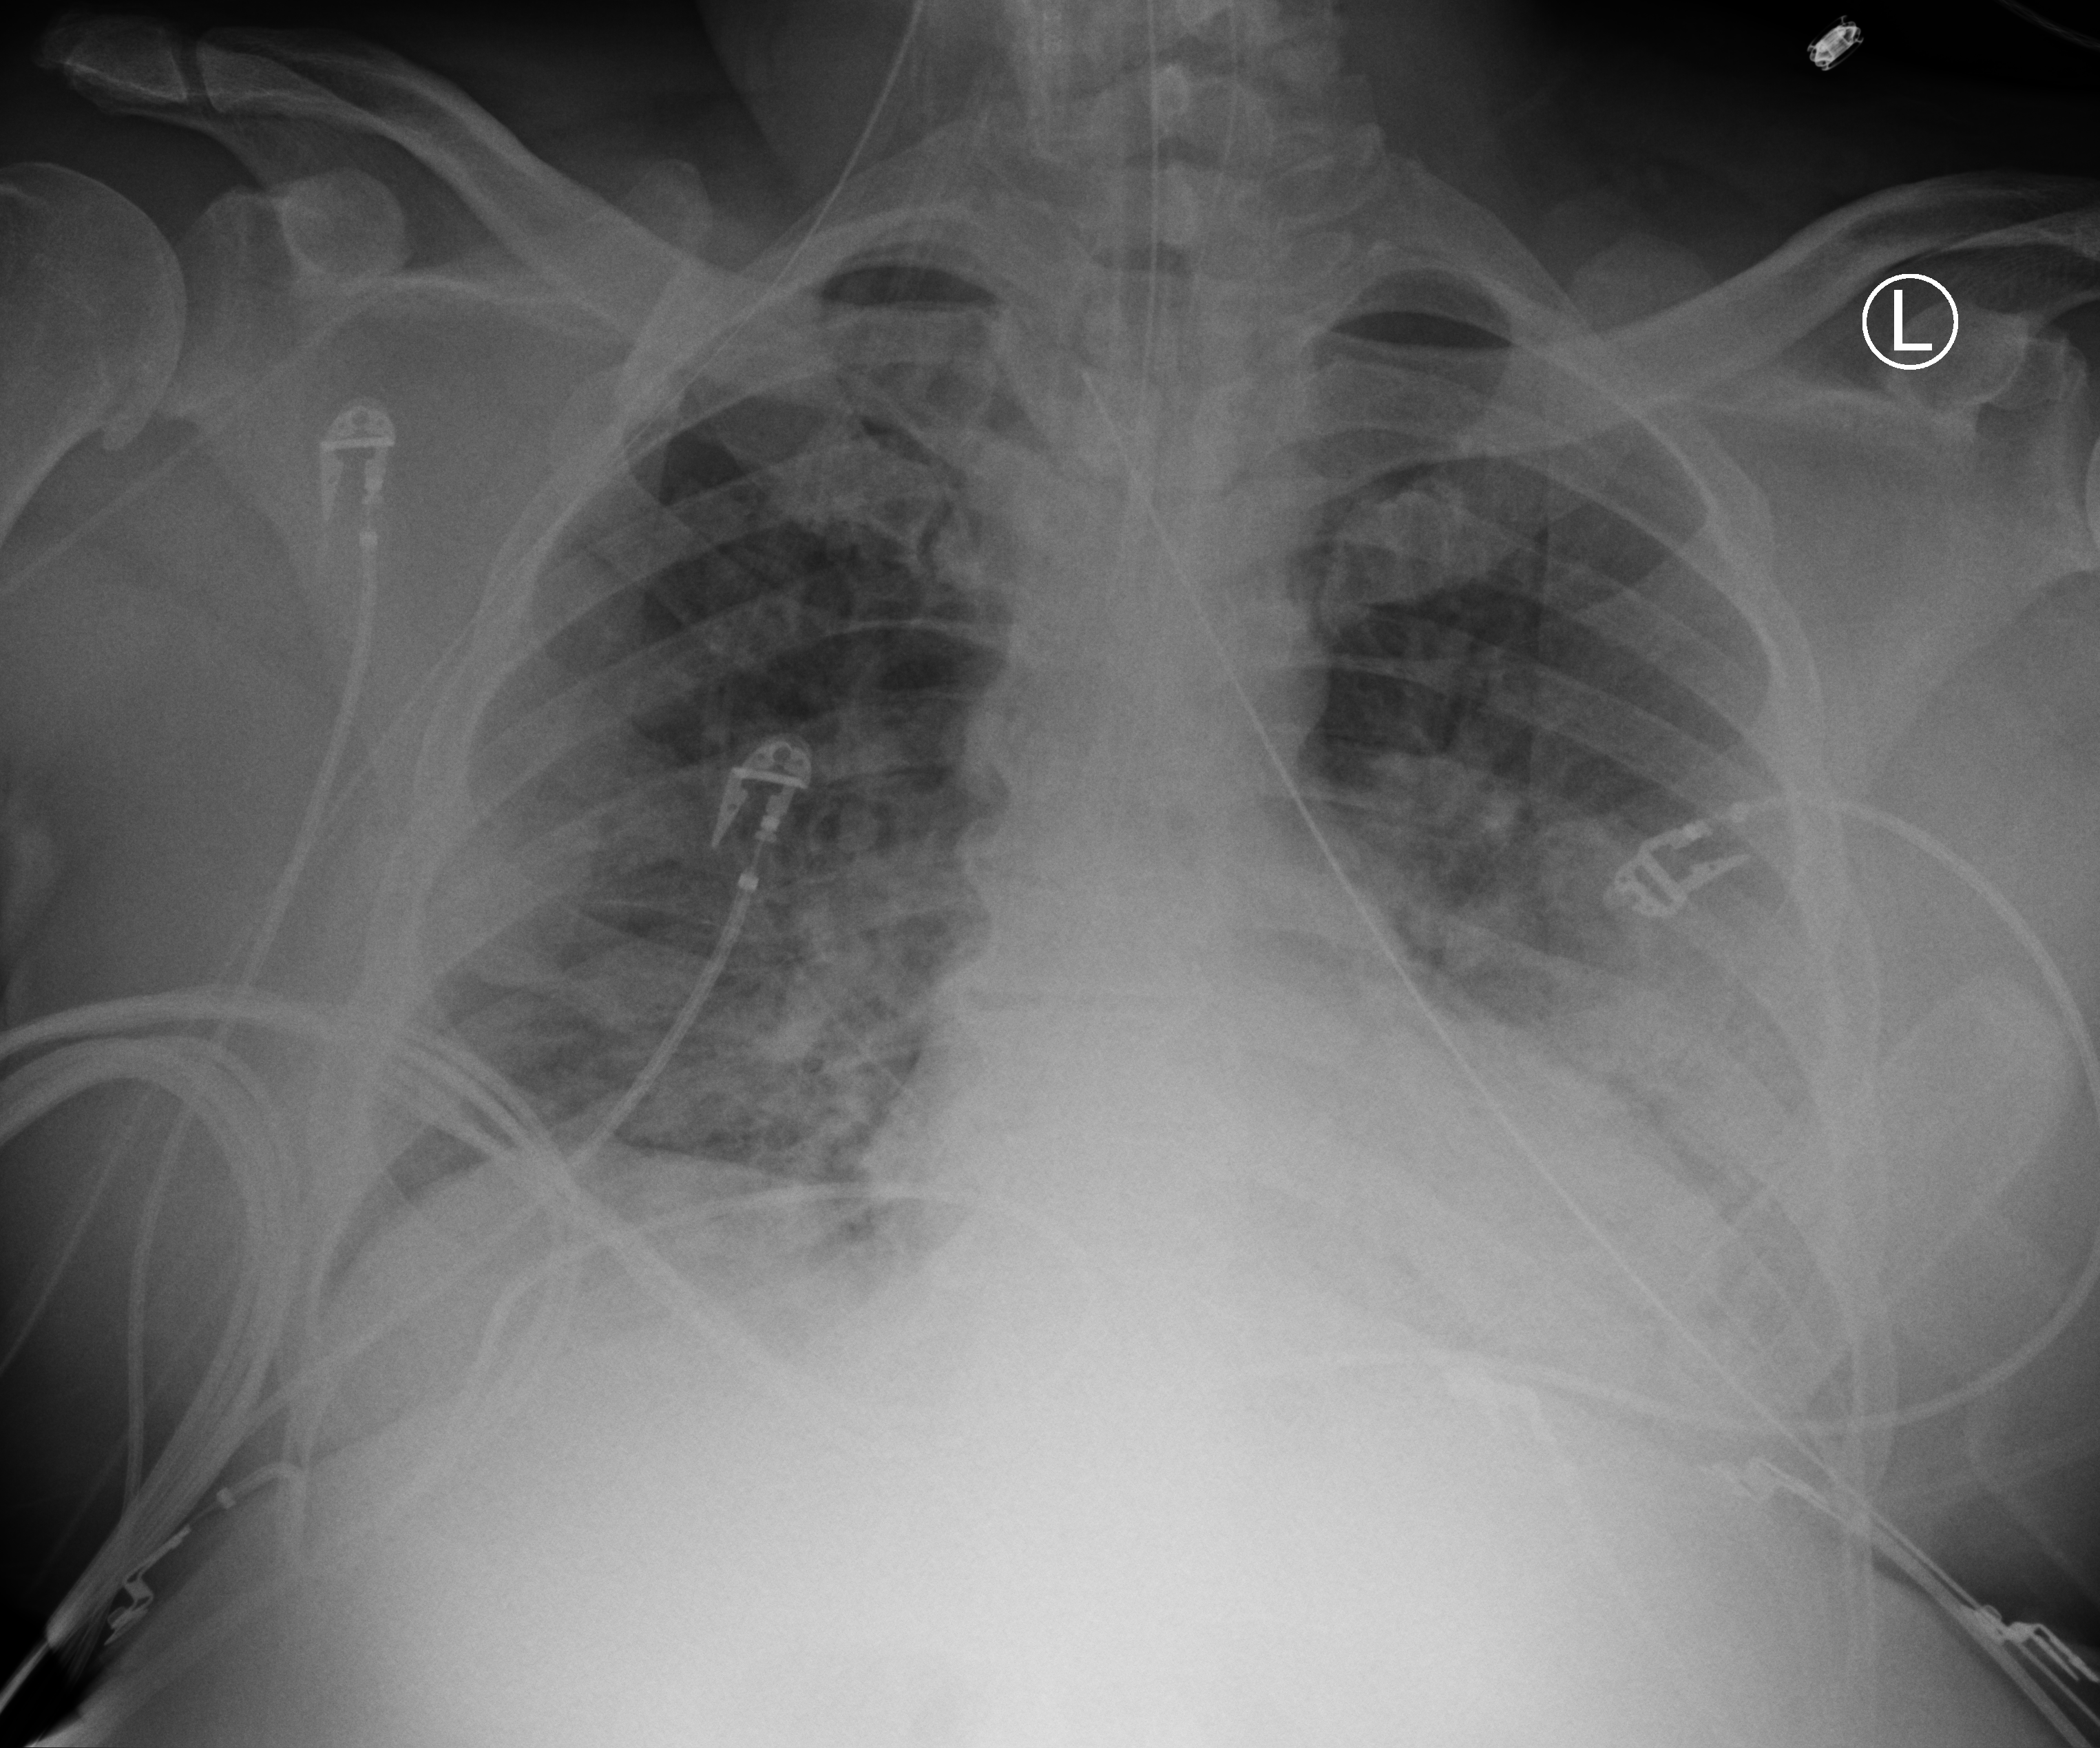
Chest X-ray (portable), anteroposterior (AP) projection. Male patient hospitalised with COVID-19, age 18–59 years.
Hospital-stay facts (about this admission, not read from this image; timing relative to this image not recorded):
- length of hospital stay: 41 days
- mechanically ventilated during this hospital stay: yes
- admitted to intensive care during this hospital stay: yes